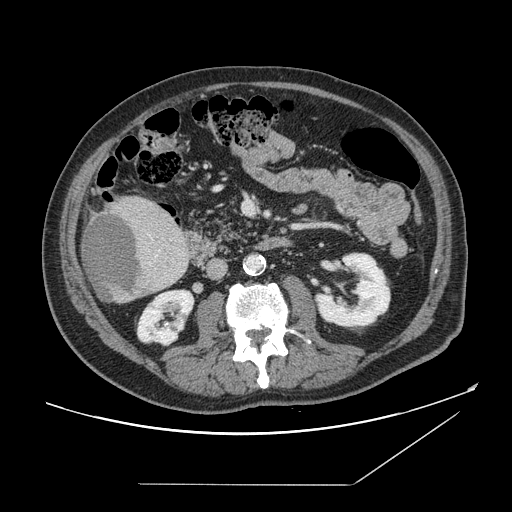
Contrast-enhanced abdominal CT, one axial slice; slice 52 of 166 in the series (ordered by position); intravenous contrast given; soft-tissue window (W 400 / L 40 HU); 2.5 mm slice thickness; 512 × 512 image matrix, field of view 416 × 416 mm. Male patient, age 80 years. Case-level facts recorded for this patient, not image findings: diagnosis: colorectal cancer liver metastases, imaged before liver resection; multiple liver metastases: no; largest metastasis: 2.2 cm; disease in both lobes: no.
Annotated regions visible in this slice (manually delineated by an expert):
- liver: box from (x=82, y=195) to (x=190, y=303) px
- liver metastasis: (x=84, y=212)–(x=141, y=301)